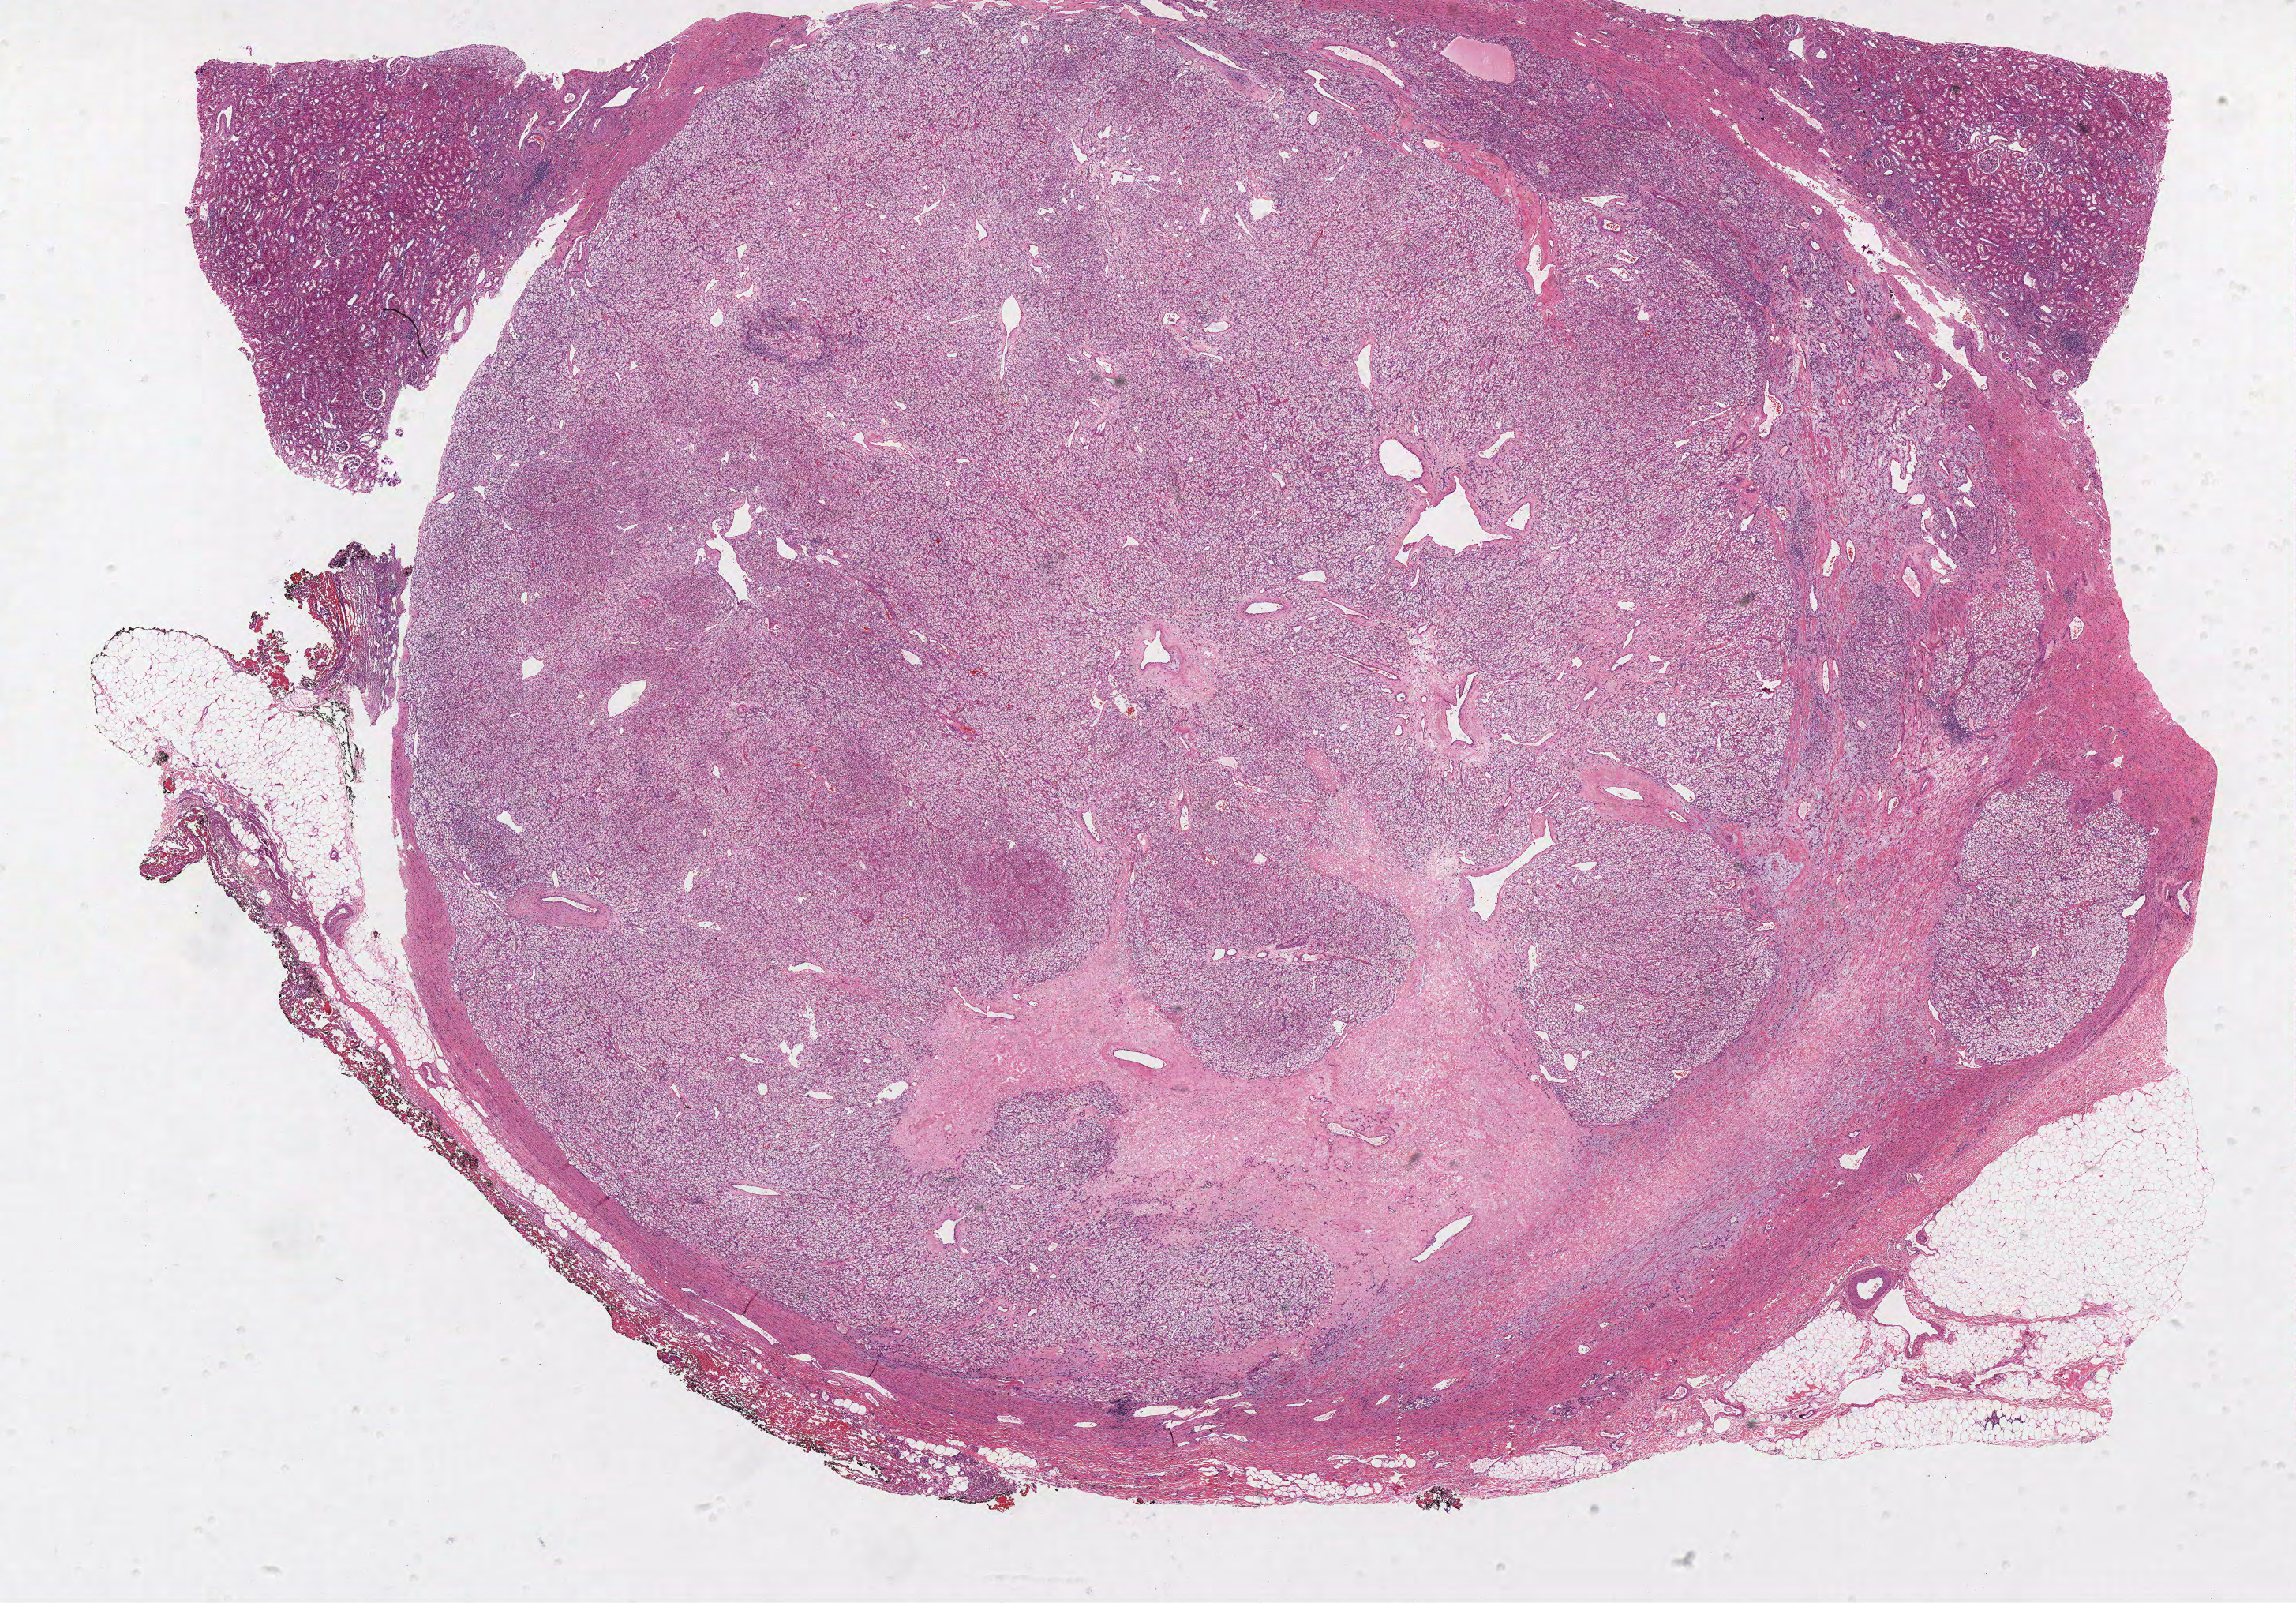
H&E whole-slide image, whole scanned area (about 23.3 x 16.2 mm, acquisition: 40x scan) shown as a low-resolution overview; formalin-fixed paraffin-embedded (FFPE) diagnostic section; sample: primary tumour, kidney. Patient: female, age at initial diagnosis 68 years.
Pathologic diagnosis: Clear cell adenocarcinoma, NOS.